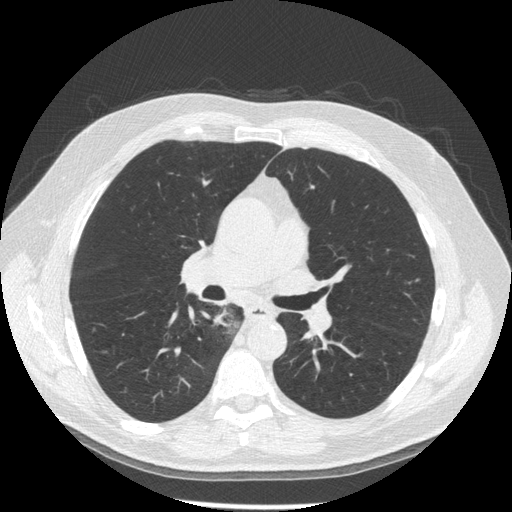
Chest CT (low-dose screening protocol), one axial image. Third annual screen. Lung window (W 1500 / L -600 HU). 1.25 mm slice thickness. Standard (soft-tissue) reconstruction kernel (STANDARD). Male, age 61 years at enrolment. Former smoker at enrolment.
Lesion marked by an expert reader, bounding box [x1, y1, x2, y2] px = [208, 298, 256, 345]. Screening reader's record for this exam: no non-calcified nodule ≥4 mm recorded. Participant outcome: lung cancer diagnosed 10 days after this screen — squamous cell carcinoma, keratinizing, NOS, right lower lobe, stage IIIB (AJCC 6th edition), 40 mm at pathology.